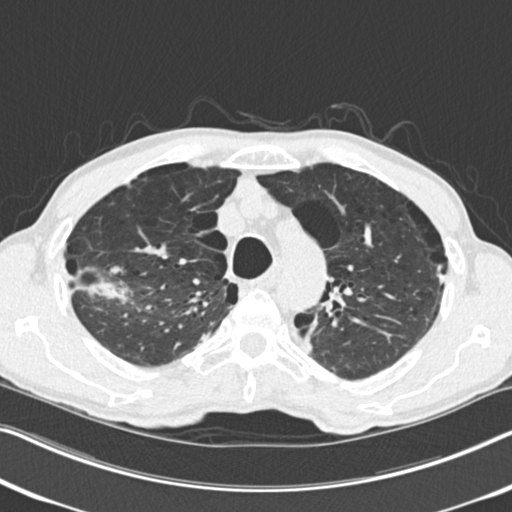
Low-dose screening chest CT, one axial slice; reconstruction kernel B30f; 120 kVp; lung window (W 1500 / L -600 HU); 2 mm slice thickness; 512 × 512 image matrix.
Annotated regions visible in this slice (manually delineated by an expert):
- lesion 1 (tumor, upper lobe of right lung): bounding box [x1, y1, x2, y2] px = [80, 267, 131, 302]